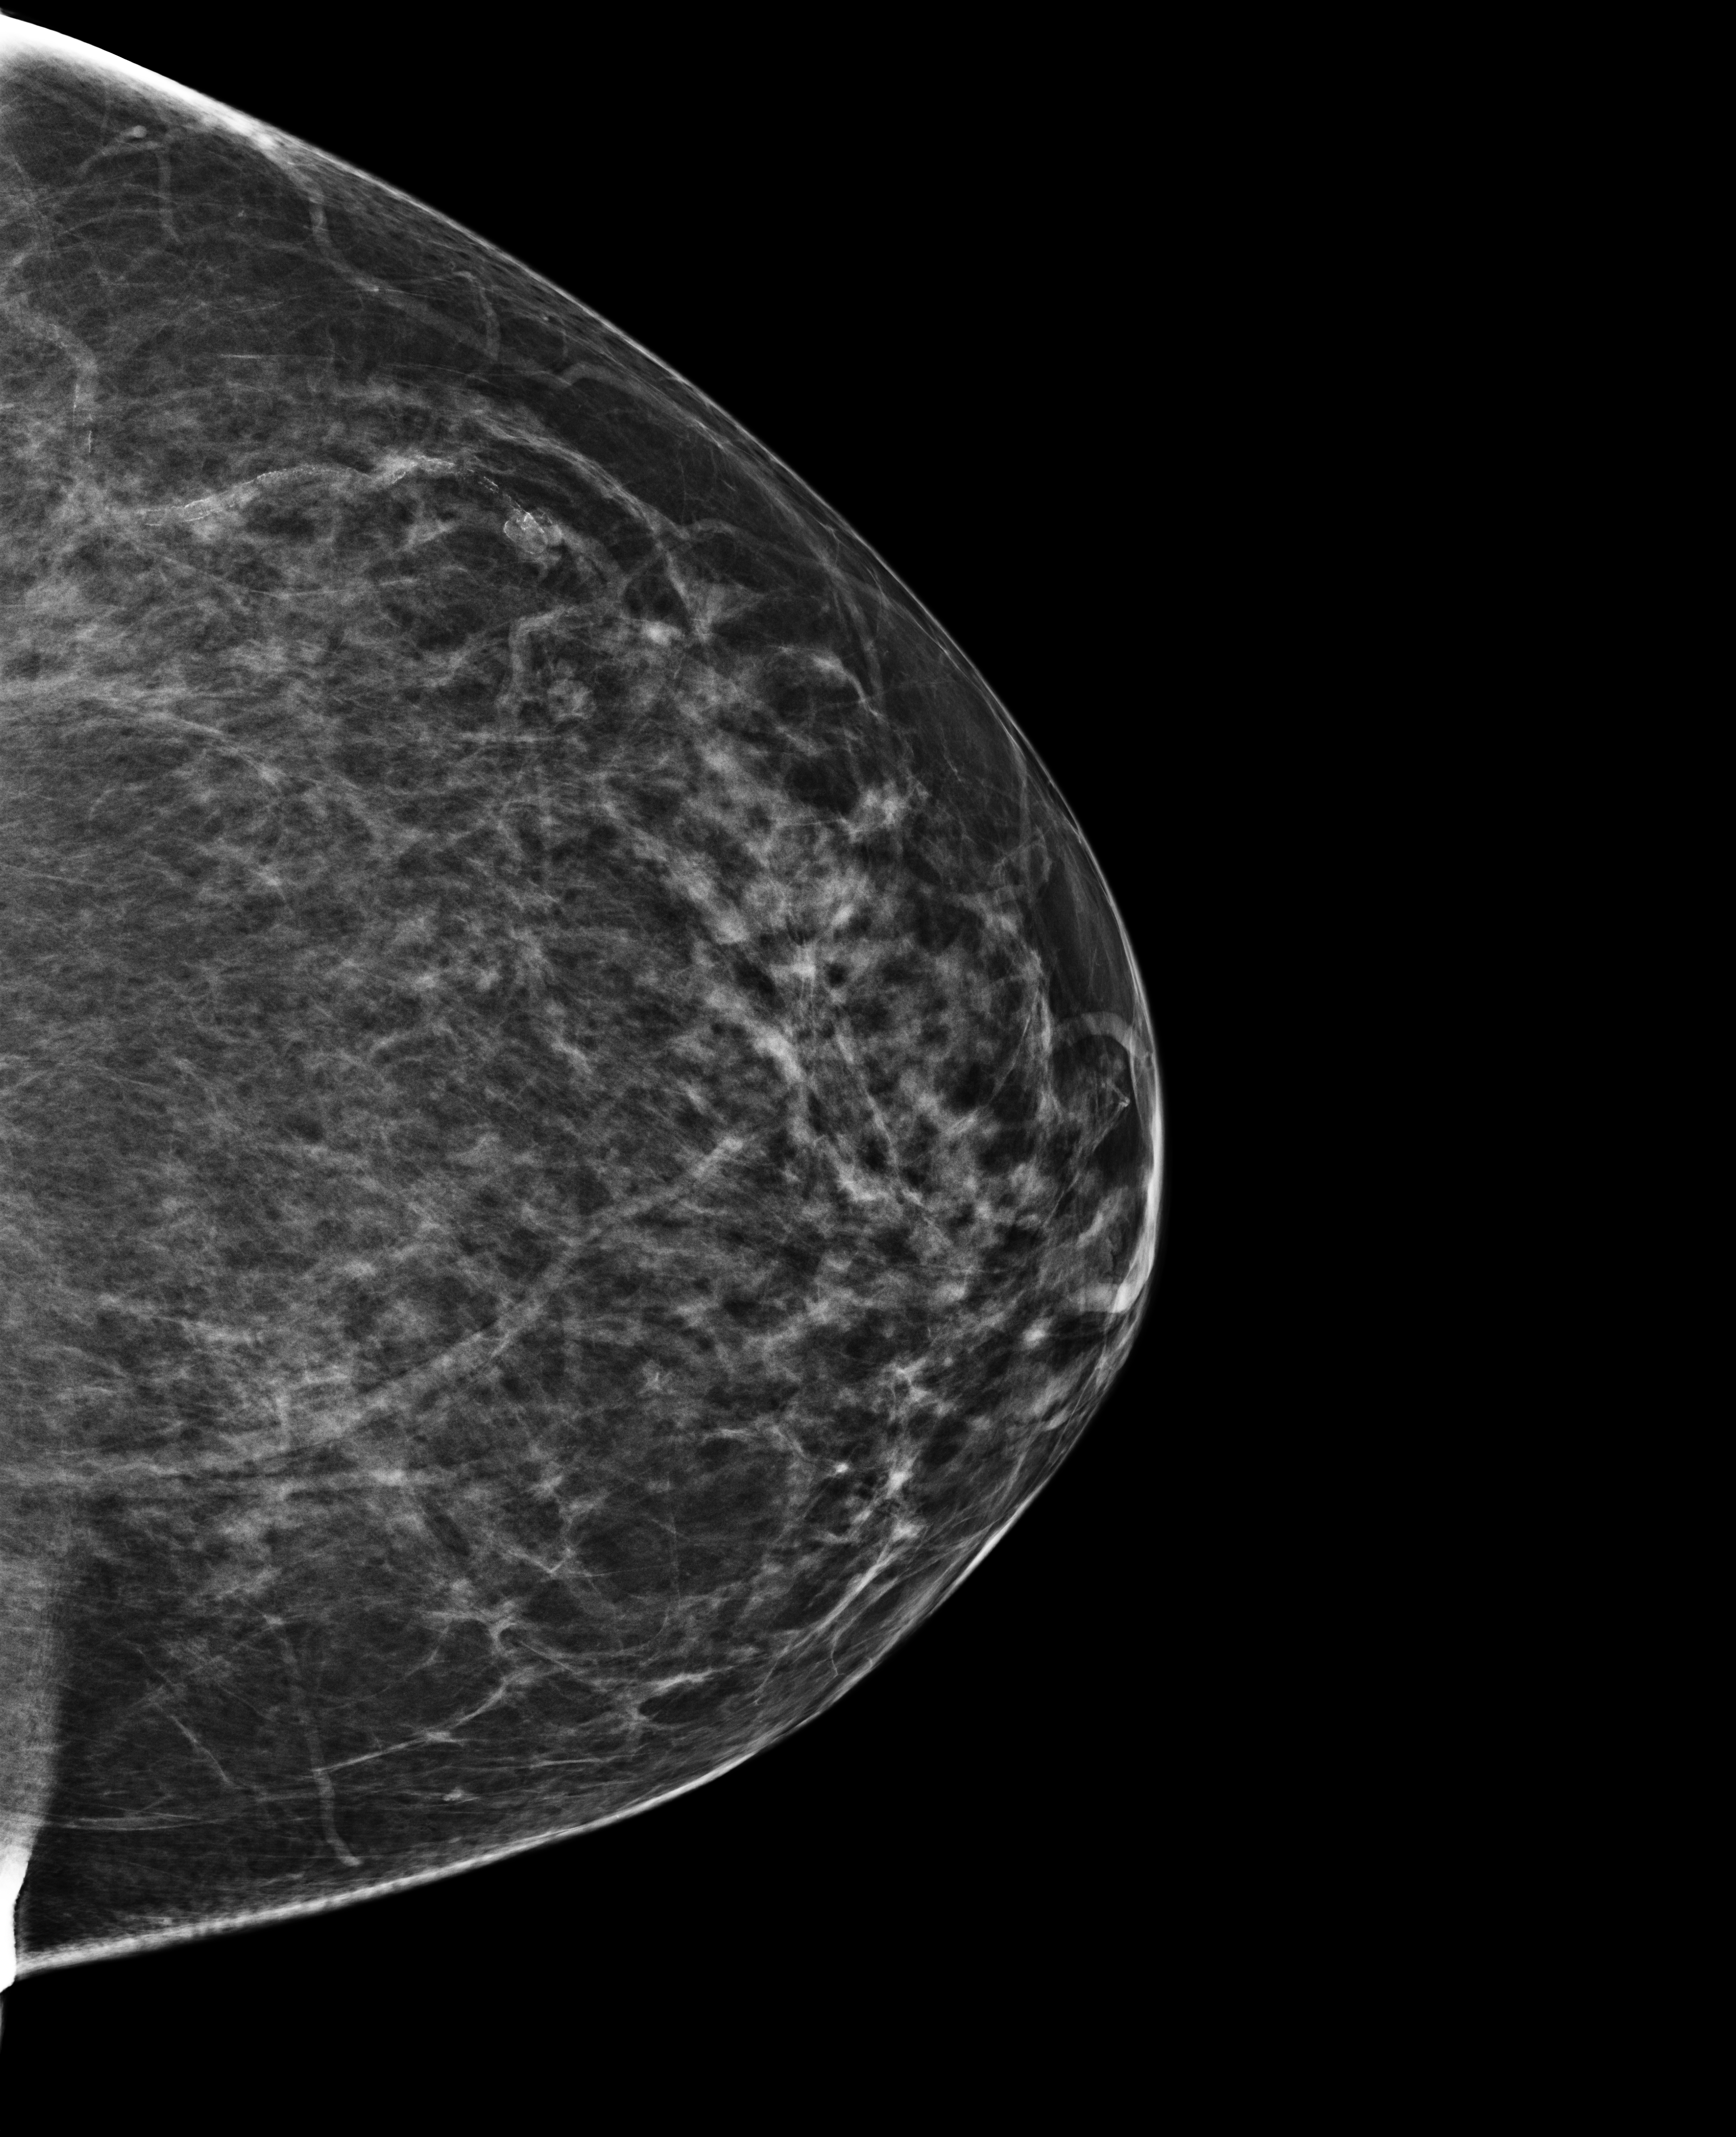
Annual screening mammography examination, compressed breast thickness 82 mm. Patient aged 68 years (female).
Image type: full-field digital mammogram. Breast: left. Projection: cranio-caudal projection.